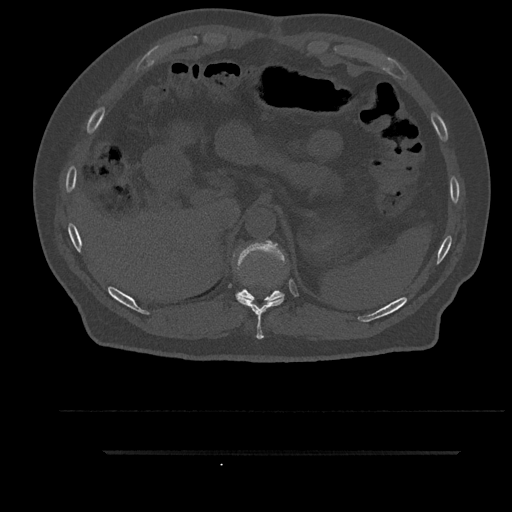
CT including the spine, one axial slice. Slice 336 of 797 in the series (ordered by position). Reconstruction kernel Br40s/3. Bone window (W 1800 / L 400 HU). 512 × 512 image matrix, field of view 432 × 432 mm. Male patient, age 63 years. From the clinical record (not read from this slice): primary cancer: renal; vertebrae with lytic lesions (as recorded): T8.
Outlined on this slice (semi-automatic segmentation, software-assisted and operator-edited):
- T10 vertebra: bounding box <236,296,284,339> (left, top, right, bottom; pixels)
- T11 vertebra: <236,240,285,304>